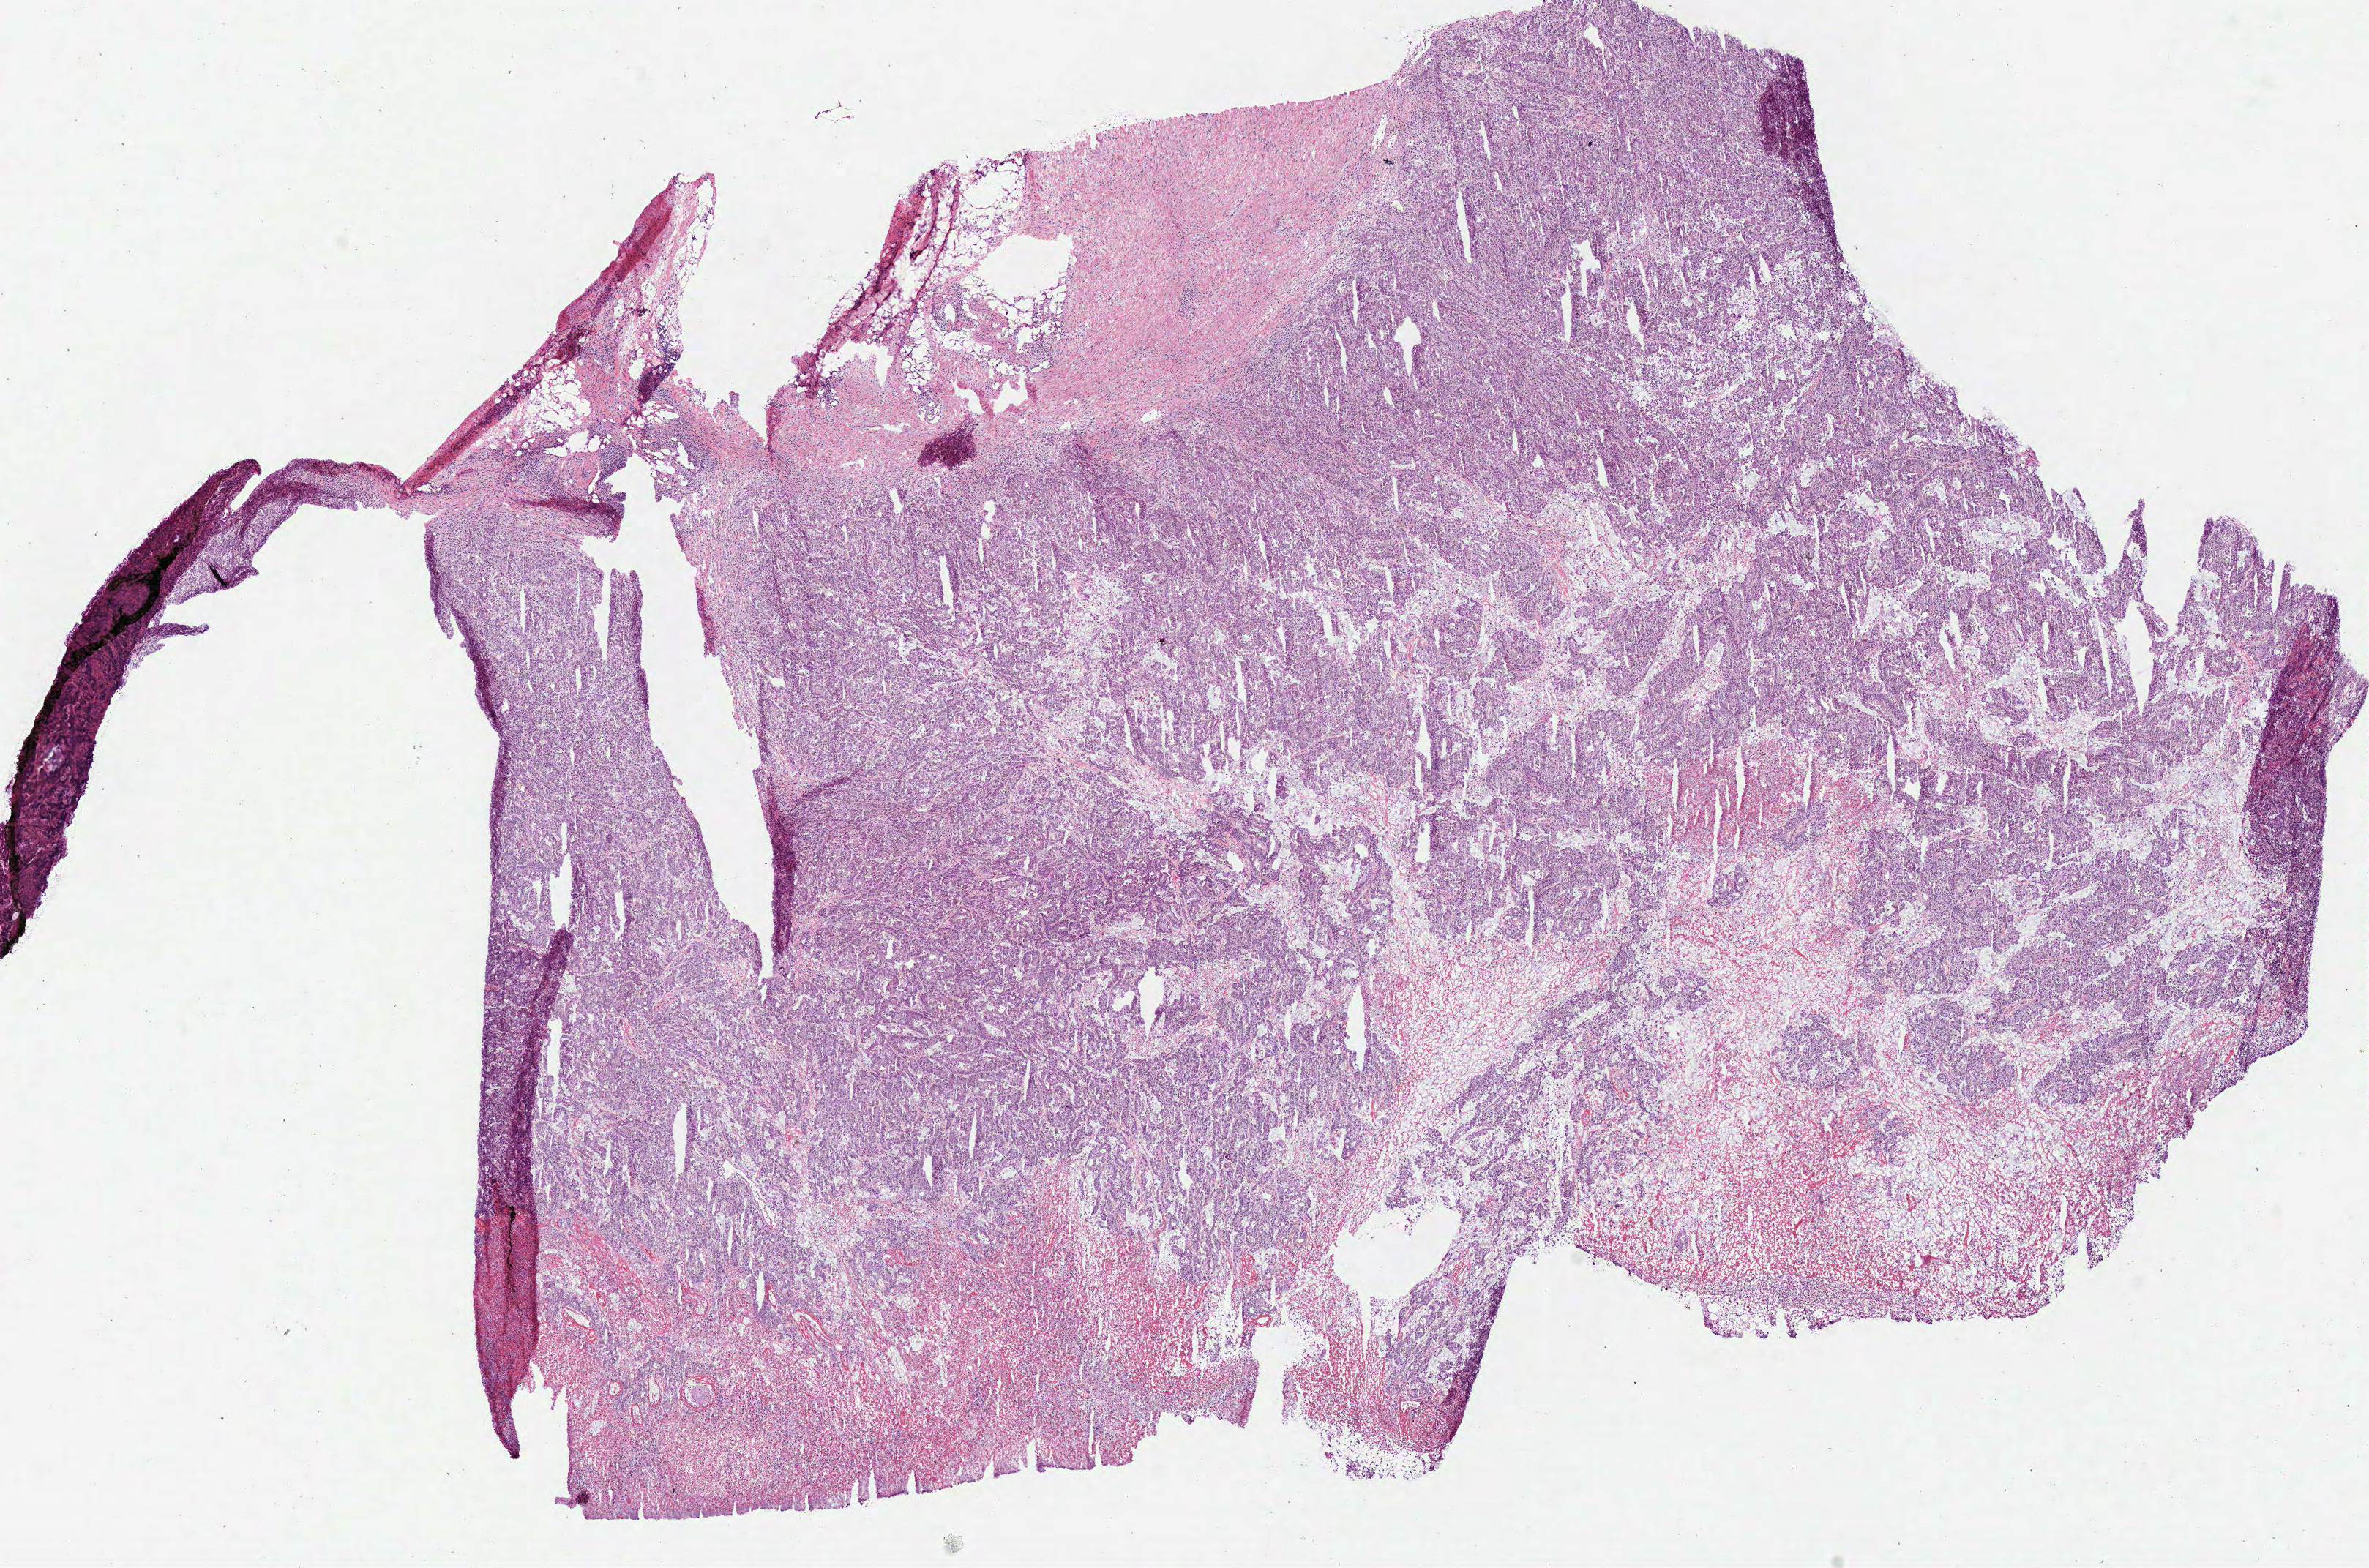
H&E-stained whole-slide image — low-resolution overview of the scanned area, about 12.7 x 8.4 mm; frozen section from the bottom of the tissue portion; sample: primary tumour, colon. Patient: male, age at initial diagnosis 74 years. Composition of this section per pathologist review: tumour cells 85%, tumour nuclei 80%.
Pathologic diagnosis: Mucinous adenocarcinoma (ascending colon).